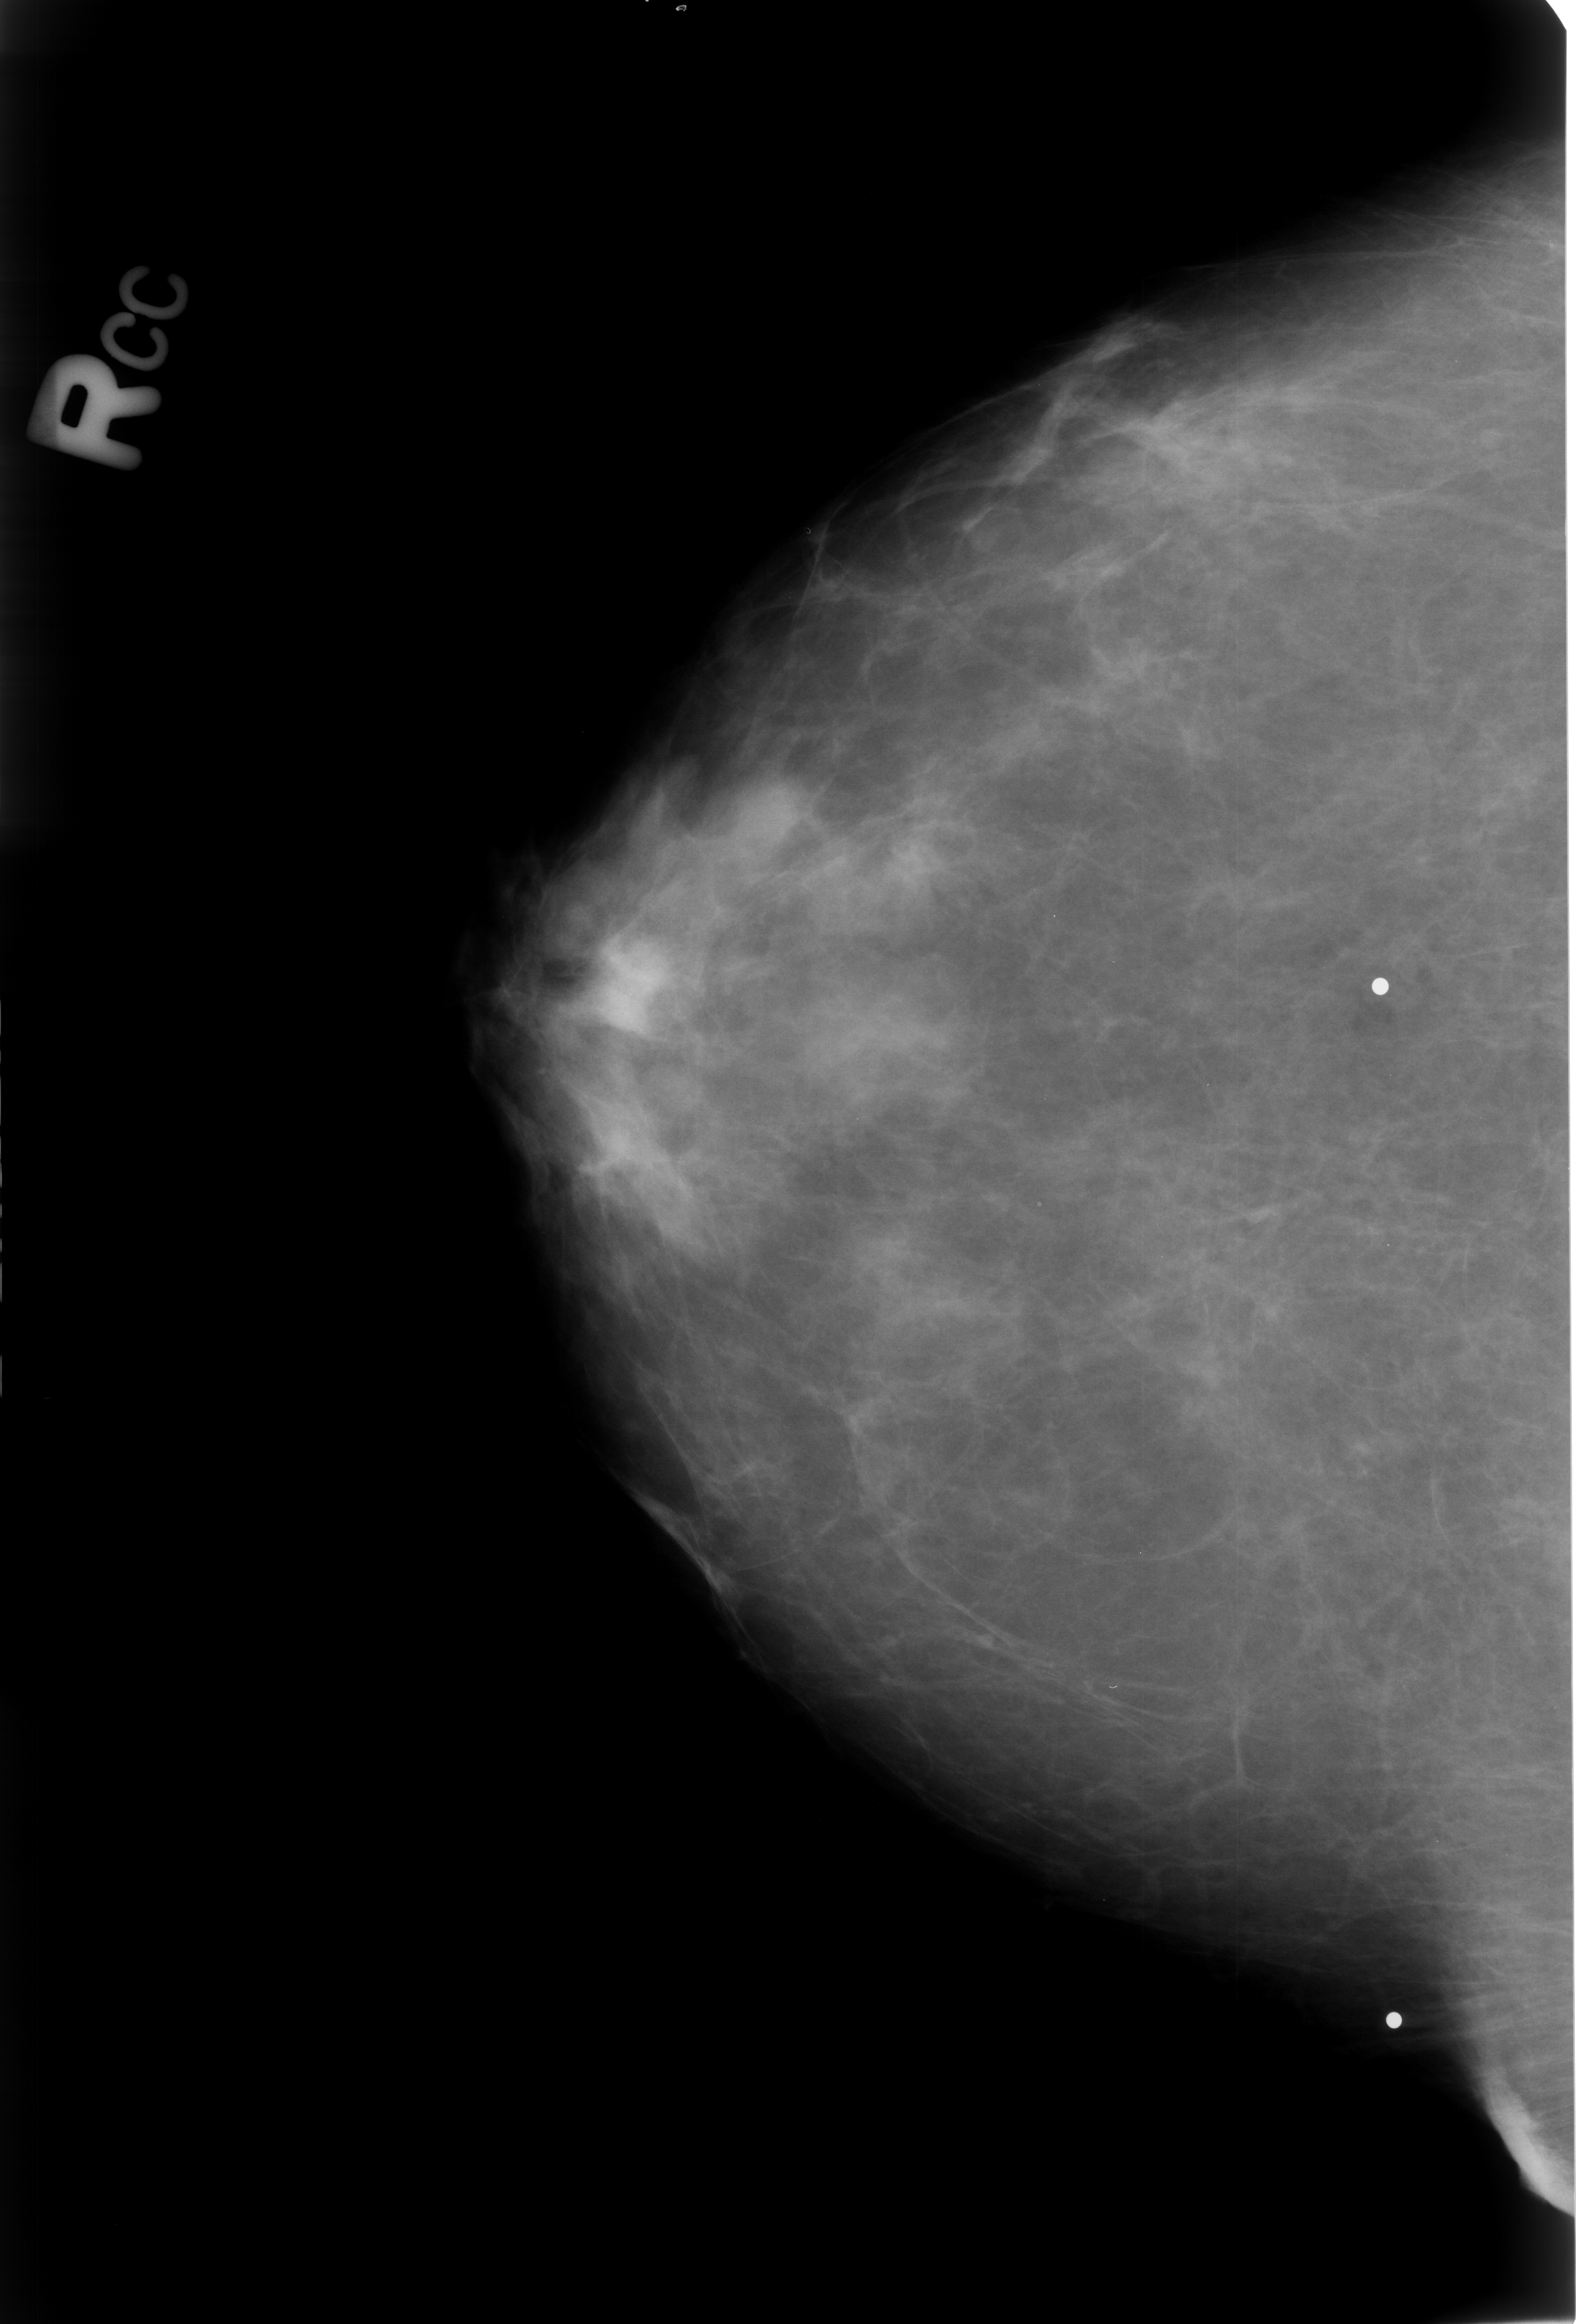
Scanned film-screen mammogram, right breast, CC view, BI-RADS breast density category 2 (scale 1–4).
- Marked findings (only marked abnormalities are described; nothing is implied about the rest of the image): calcifications, morphology punctate; BI-RADS assessment category 2; subtlety rating 3 on a 1 (subtle) to 5 (obvious) scale; benign; no additional work-up was recommended (benign without callback).